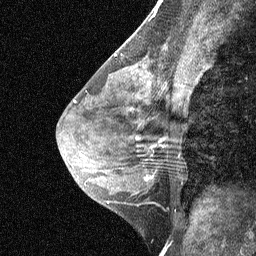
Breast MRI (dynamic contrast-enhanced), one sagittal slice; slice 35 of 64 in the series (ordered by position); dynamic contrast-enhanced study with each time point stored as its own series, time point 3 of 4 at this slice position (ordered by acquisition time); 1.5 T; TE 4.8 ms, TR 27 ms; 2 mm slice thickness; 256 × 256 image matrix, field of view 180 × 180 mm. Female patient, age 44 years. From the clinical record (not read from this slice): setting: breast cancer imaged before/during neoadjuvant chemotherapy; receptor status: HR-positive, HER2-negative.
Outlined on this slice (semi-automatic segmentation, software-assisted and operator-edited):
- analysis volume of interest (the breast-tissue region the enhancement analysis was run in; not a lesion): bounding box [x1, y1, x2, y2] px = [115, 117, 185, 188]
- tumour enhancement mask (voxels above the 90 % enhancement threshold inside the analysis volume of interest): [145, 177, 150, 180]